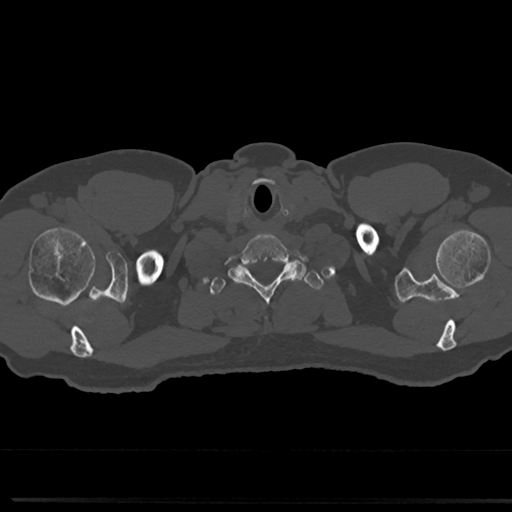
CT including the spine, one axial slice; reconstruction kernel Br40s/3; bone window (W 1800 / L 400 HU); 0.5 mm slice thickness; 512 × 512 image matrix. Male patient, age 61 years. From the clinical record (not read from this slice): primary cancer: prostate.
Structures marked on this image (semi-automatic segmentation, software-assisted and operator-edited):
- T1 vertebra: box from (x=209, y=265) to (x=319, y=295) px